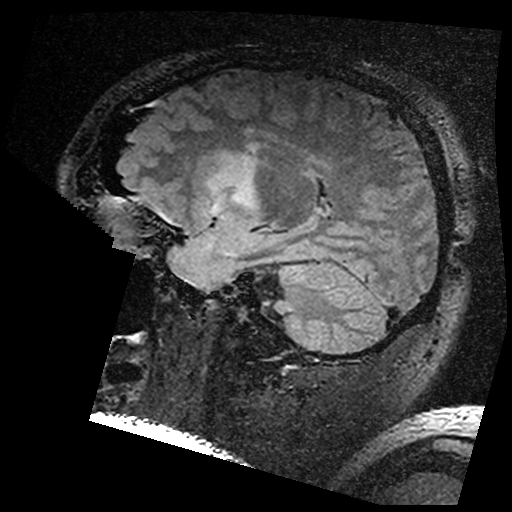
Brain MRI from a brain-tumour surgery series, one sagittal slice. Position 113 of 176 along the scan axis. T2 FLAIR. 512 × 512 image matrix, field of view 250 × 250 mm. From the clinical record (not read from this slice): histopathology: Astrocytoma; WHO grade: 3; IDH mutation: yes.
Structures marked on this image (outlined manually by an expert reader):
- residual tumour: box from (x=202, y=147) to (x=260, y=200) px